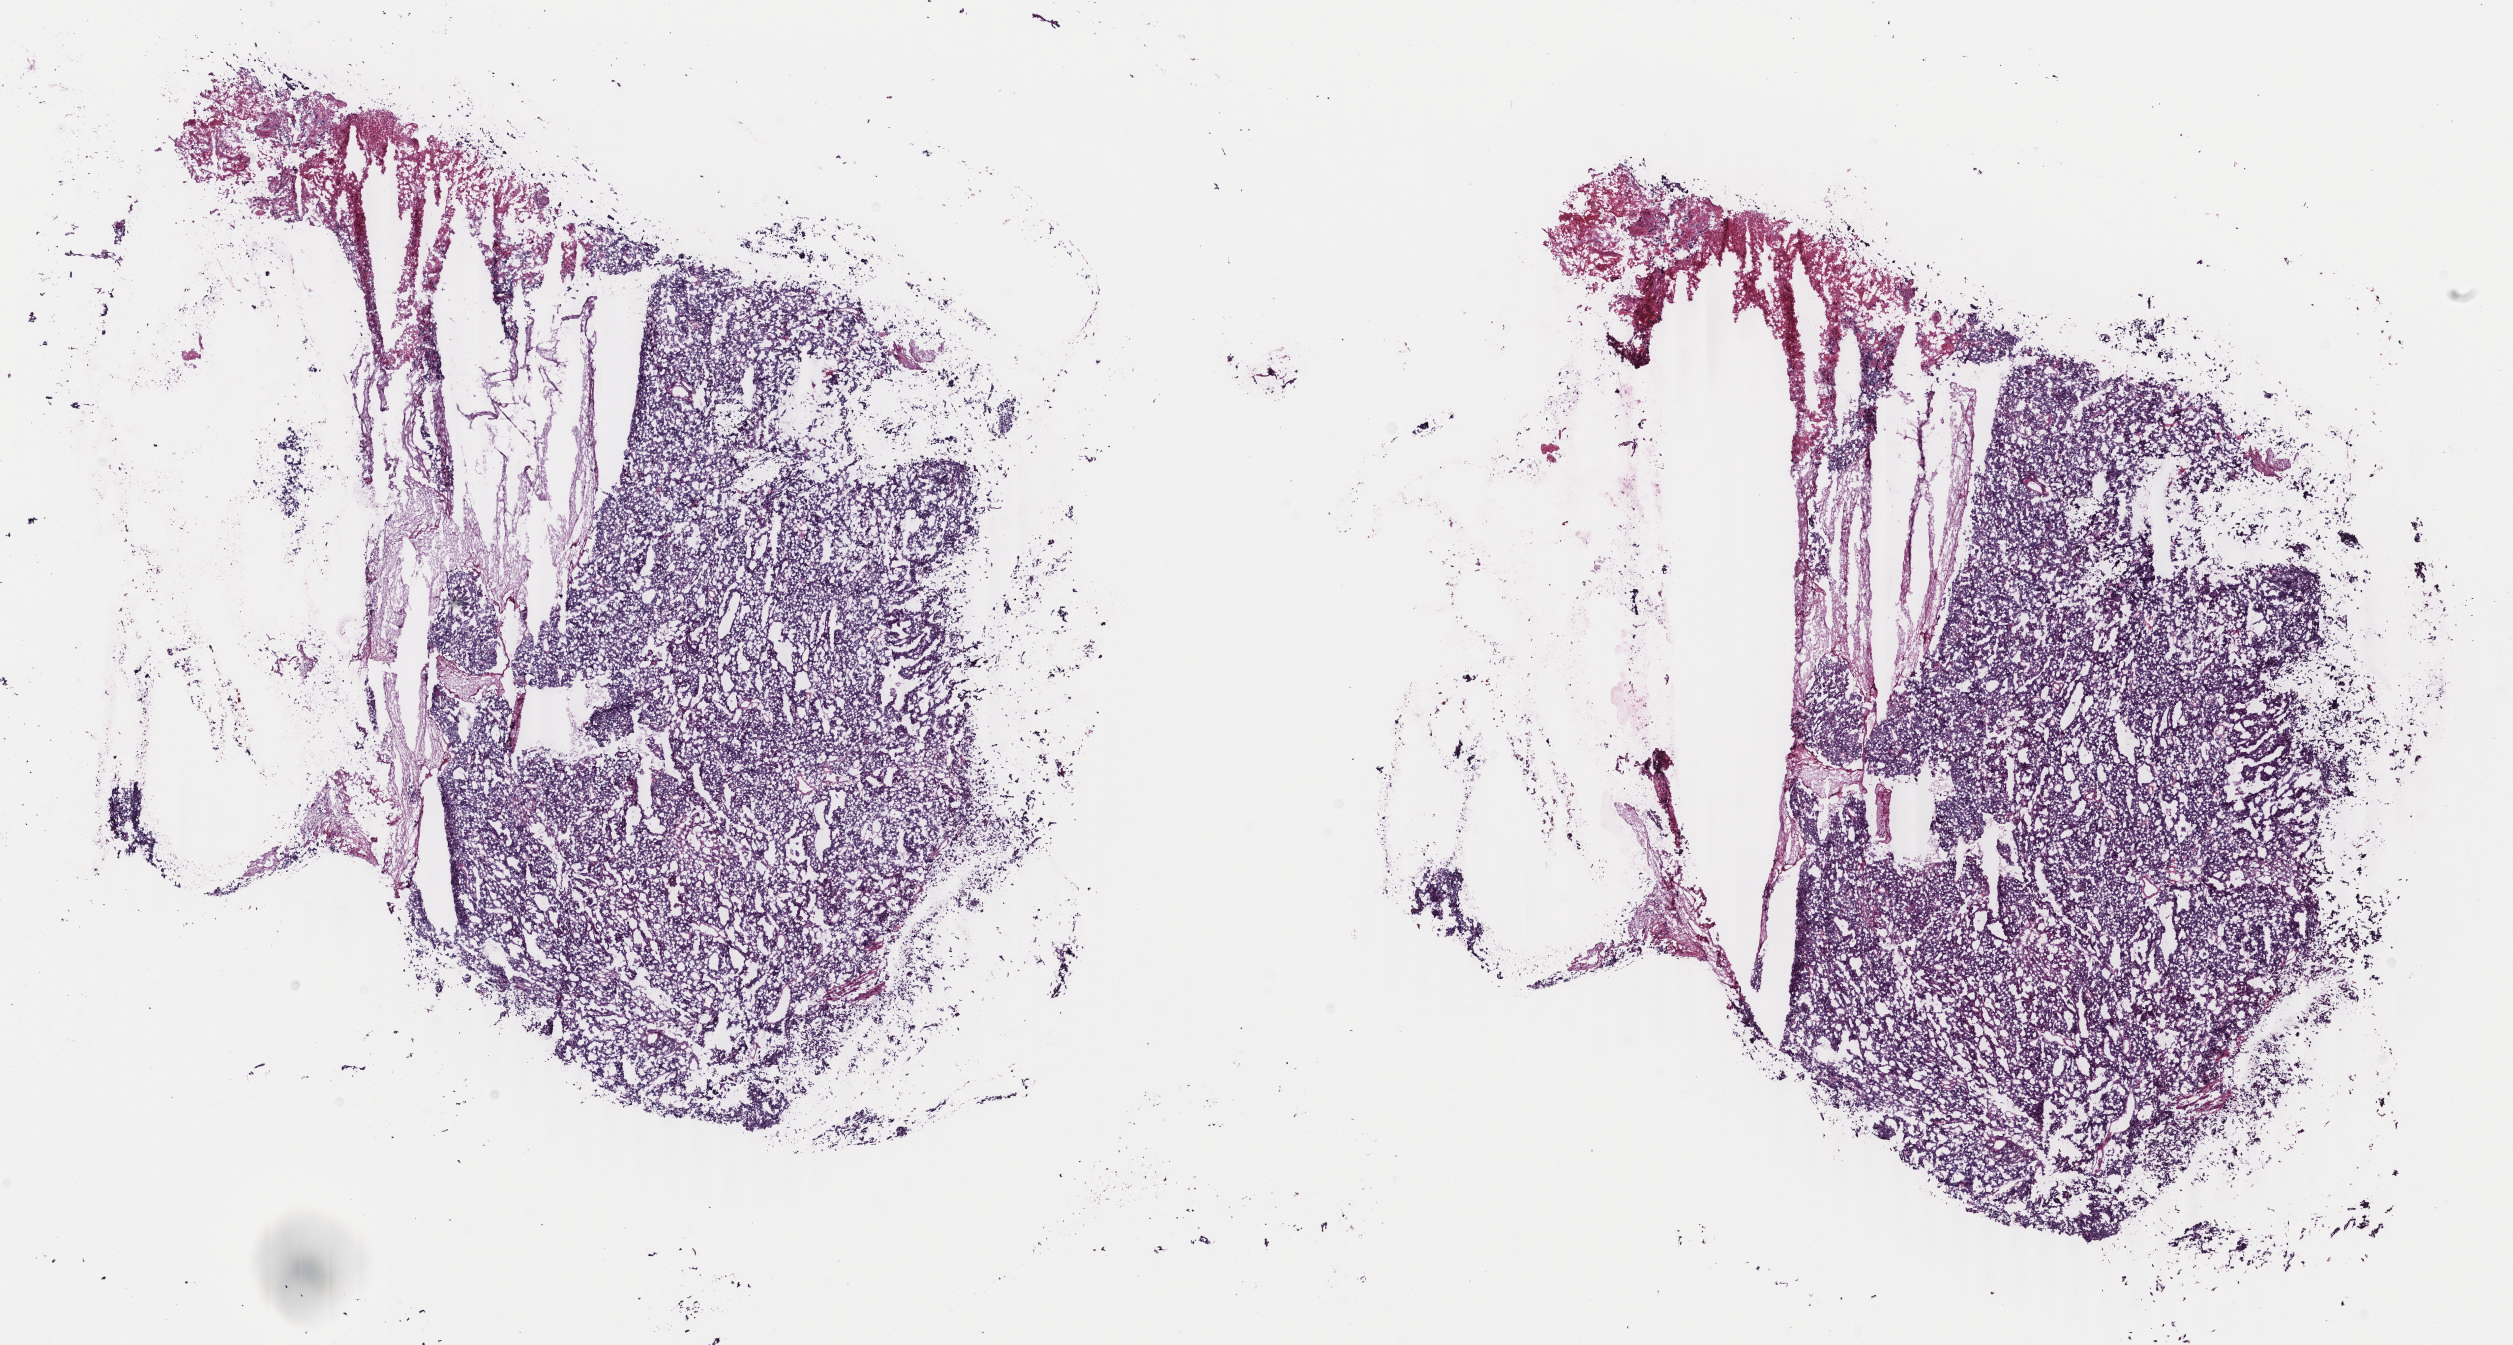
H&E whole-slide image, a low-resolution overview of the entire scanned area, about 20.0 x 10.7 mm, frozen section from the top of the tissue portion, primary tumour sample from the uterus. Female, age 59 years at initial diagnosis. Histologic grade: G3 (poorly differentiated). Slide review estimates, as recorded: tumour cells 80%, tumour nuclei 80%, normal cells 0%, stromal cells 5%, necrosis 15%. Inflammatory infiltration, as recorded: lymphocyte infiltration 1%, monocyte infiltration 0%, neutrophil infiltration 1%.
- pathologic diagnosis: Endometrioid adenocarcinoma, NOS (endometrium)
- FIGO stage: IIA
- lymph nodes positive (case pathology): 0 of 34 examined